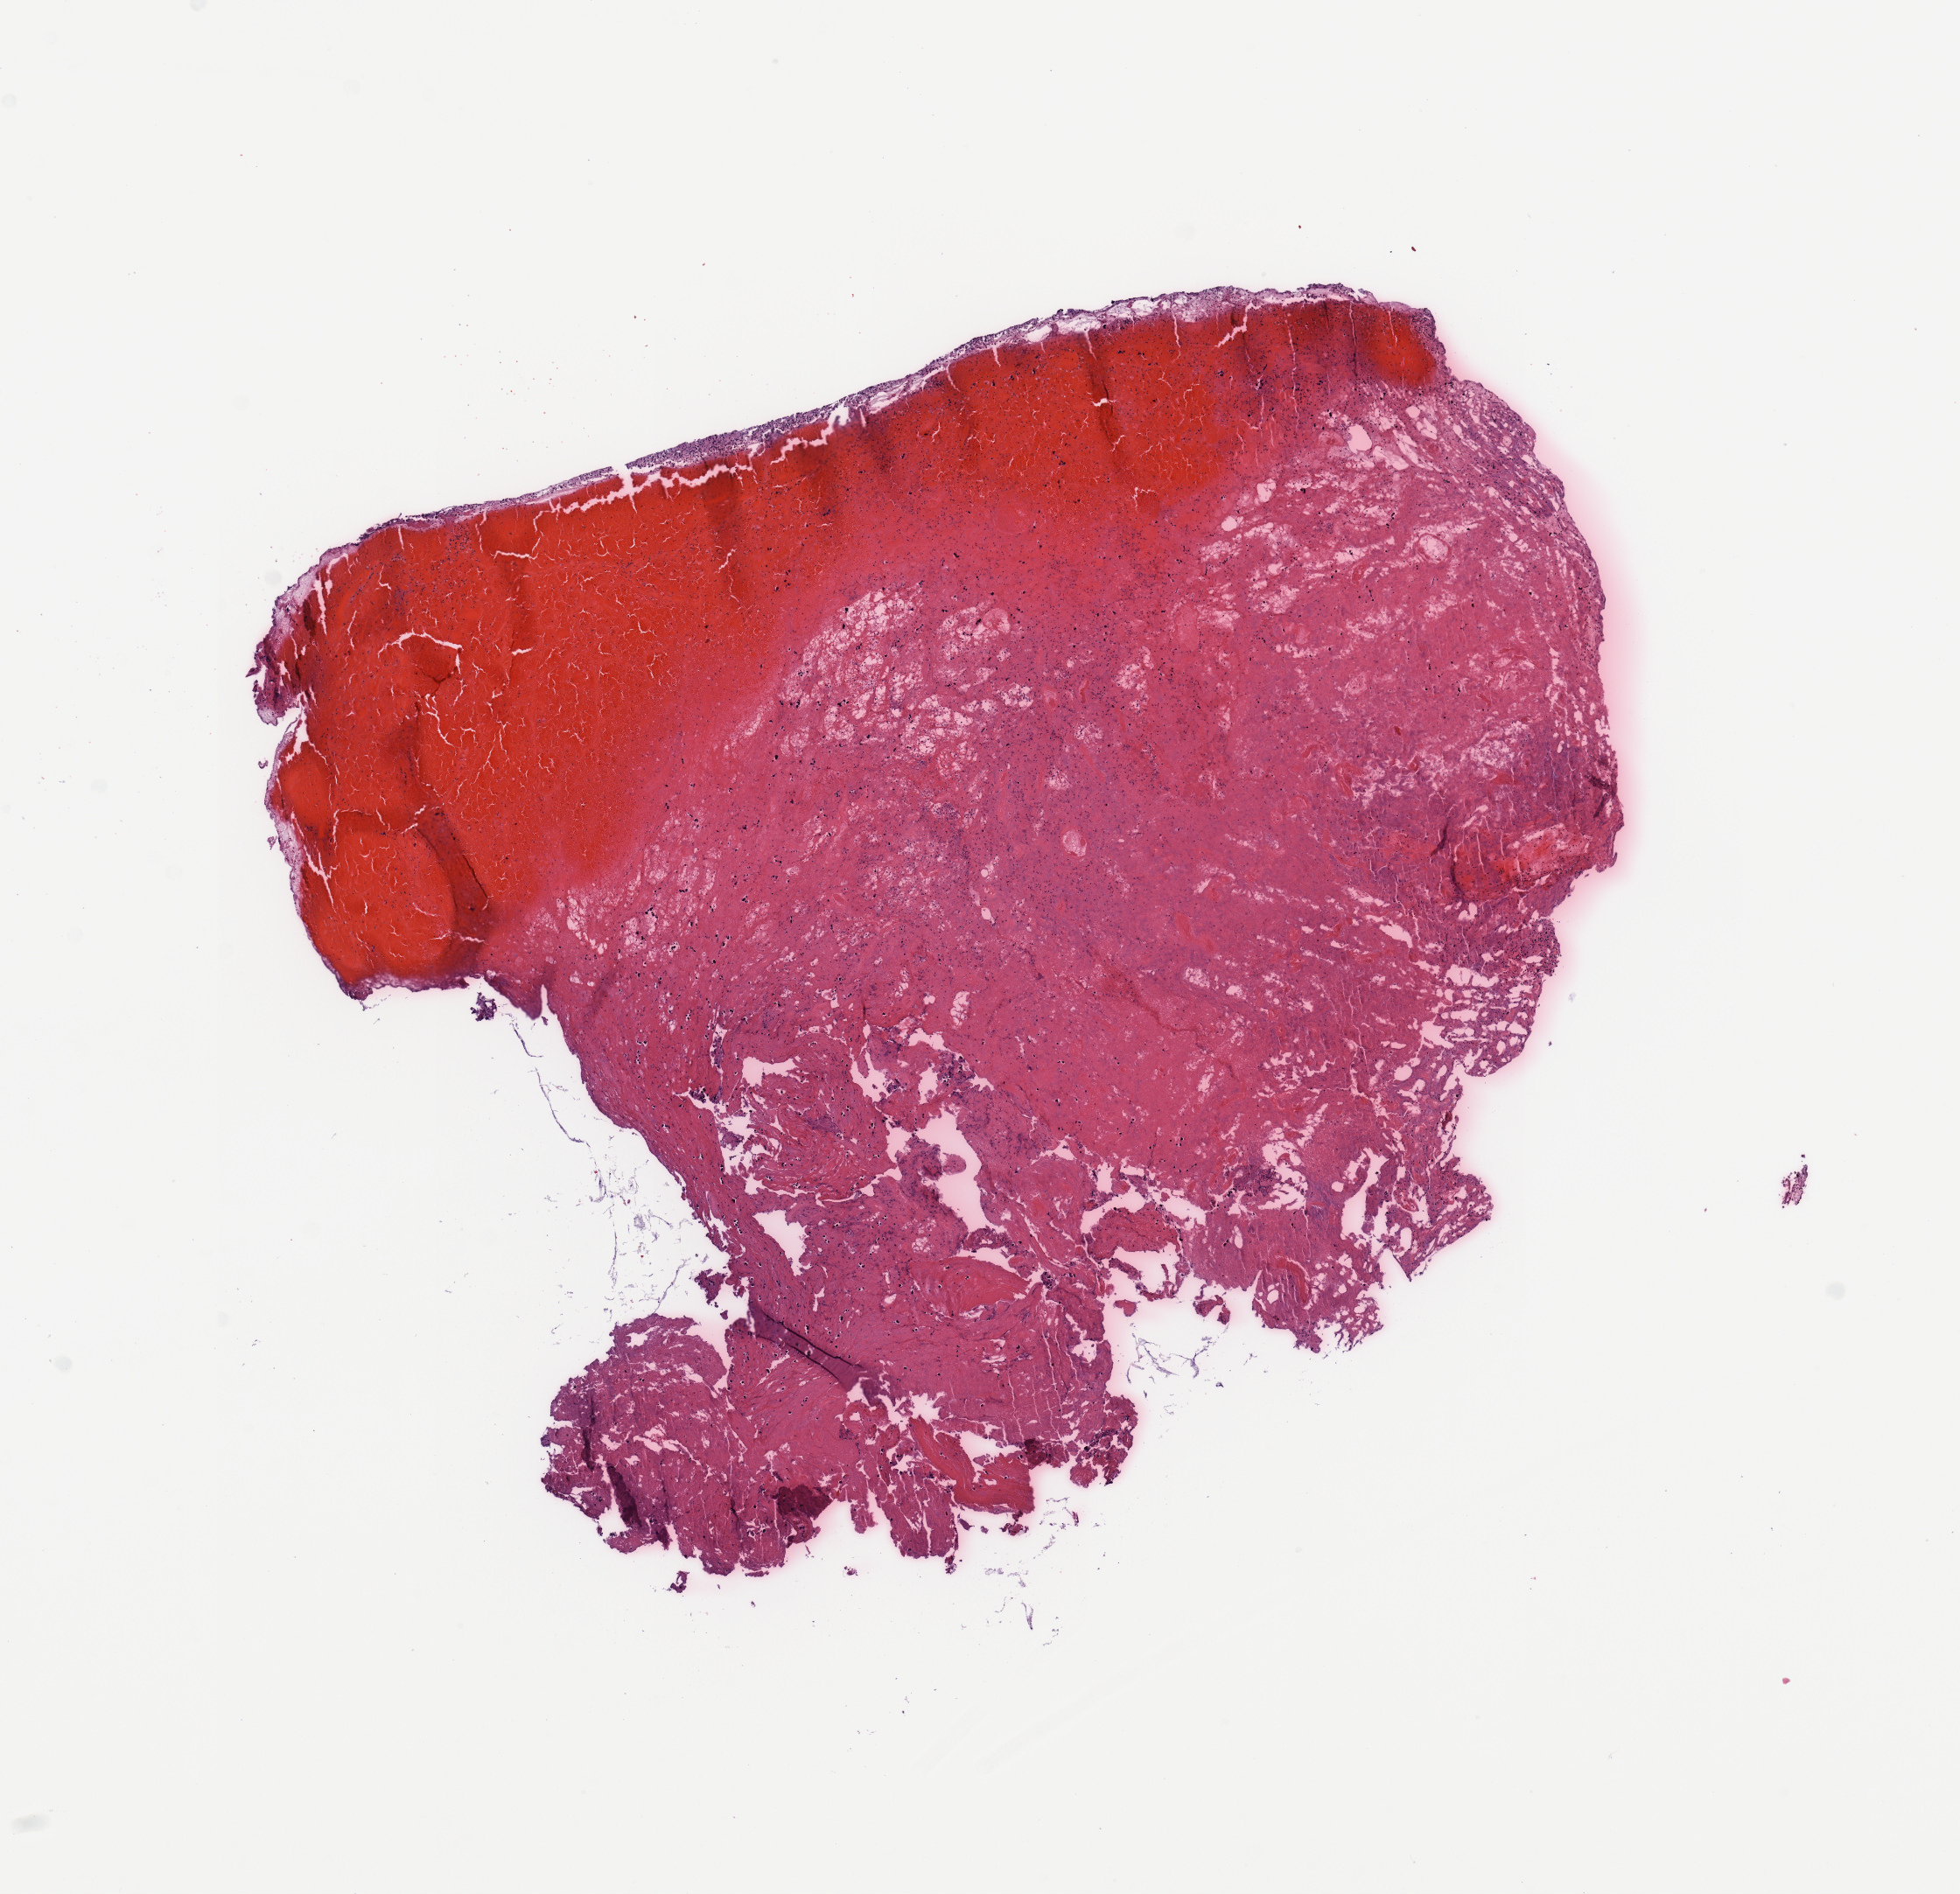
Whole-slide histology image, H&E-stained — shown as a low-resolution overview of the whole scanned area (about 8.9 x 8.6 mm), tumour tissue sample, brain. Female, 59 y/o.
Histologic diagnosis: Glioblastoma.